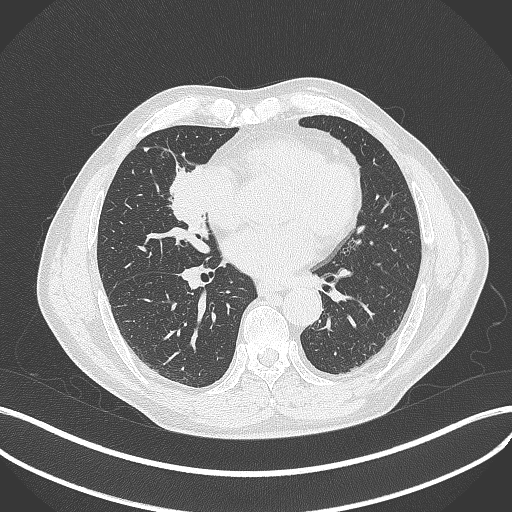
Chest CT, one axial slice; position 180 of 429 along the scan axis; reconstruction kernel B70f; 120 kVp; lung window (W 1500 / L -600 HU); 512 × 512 image matrix, field of view 400 × 400 mm. Patient: male, 61 years. From the clinical record (not read from this slice): clinical TNM (as recorded): T2b N1 M0.
Outlined on this slice (rectangle marked by the reading radiologist):
- lung tumour (recorded histology: squamous cell carcinoma): bounding box <162,157,213,244> (left, top, right, bottom; pixels)